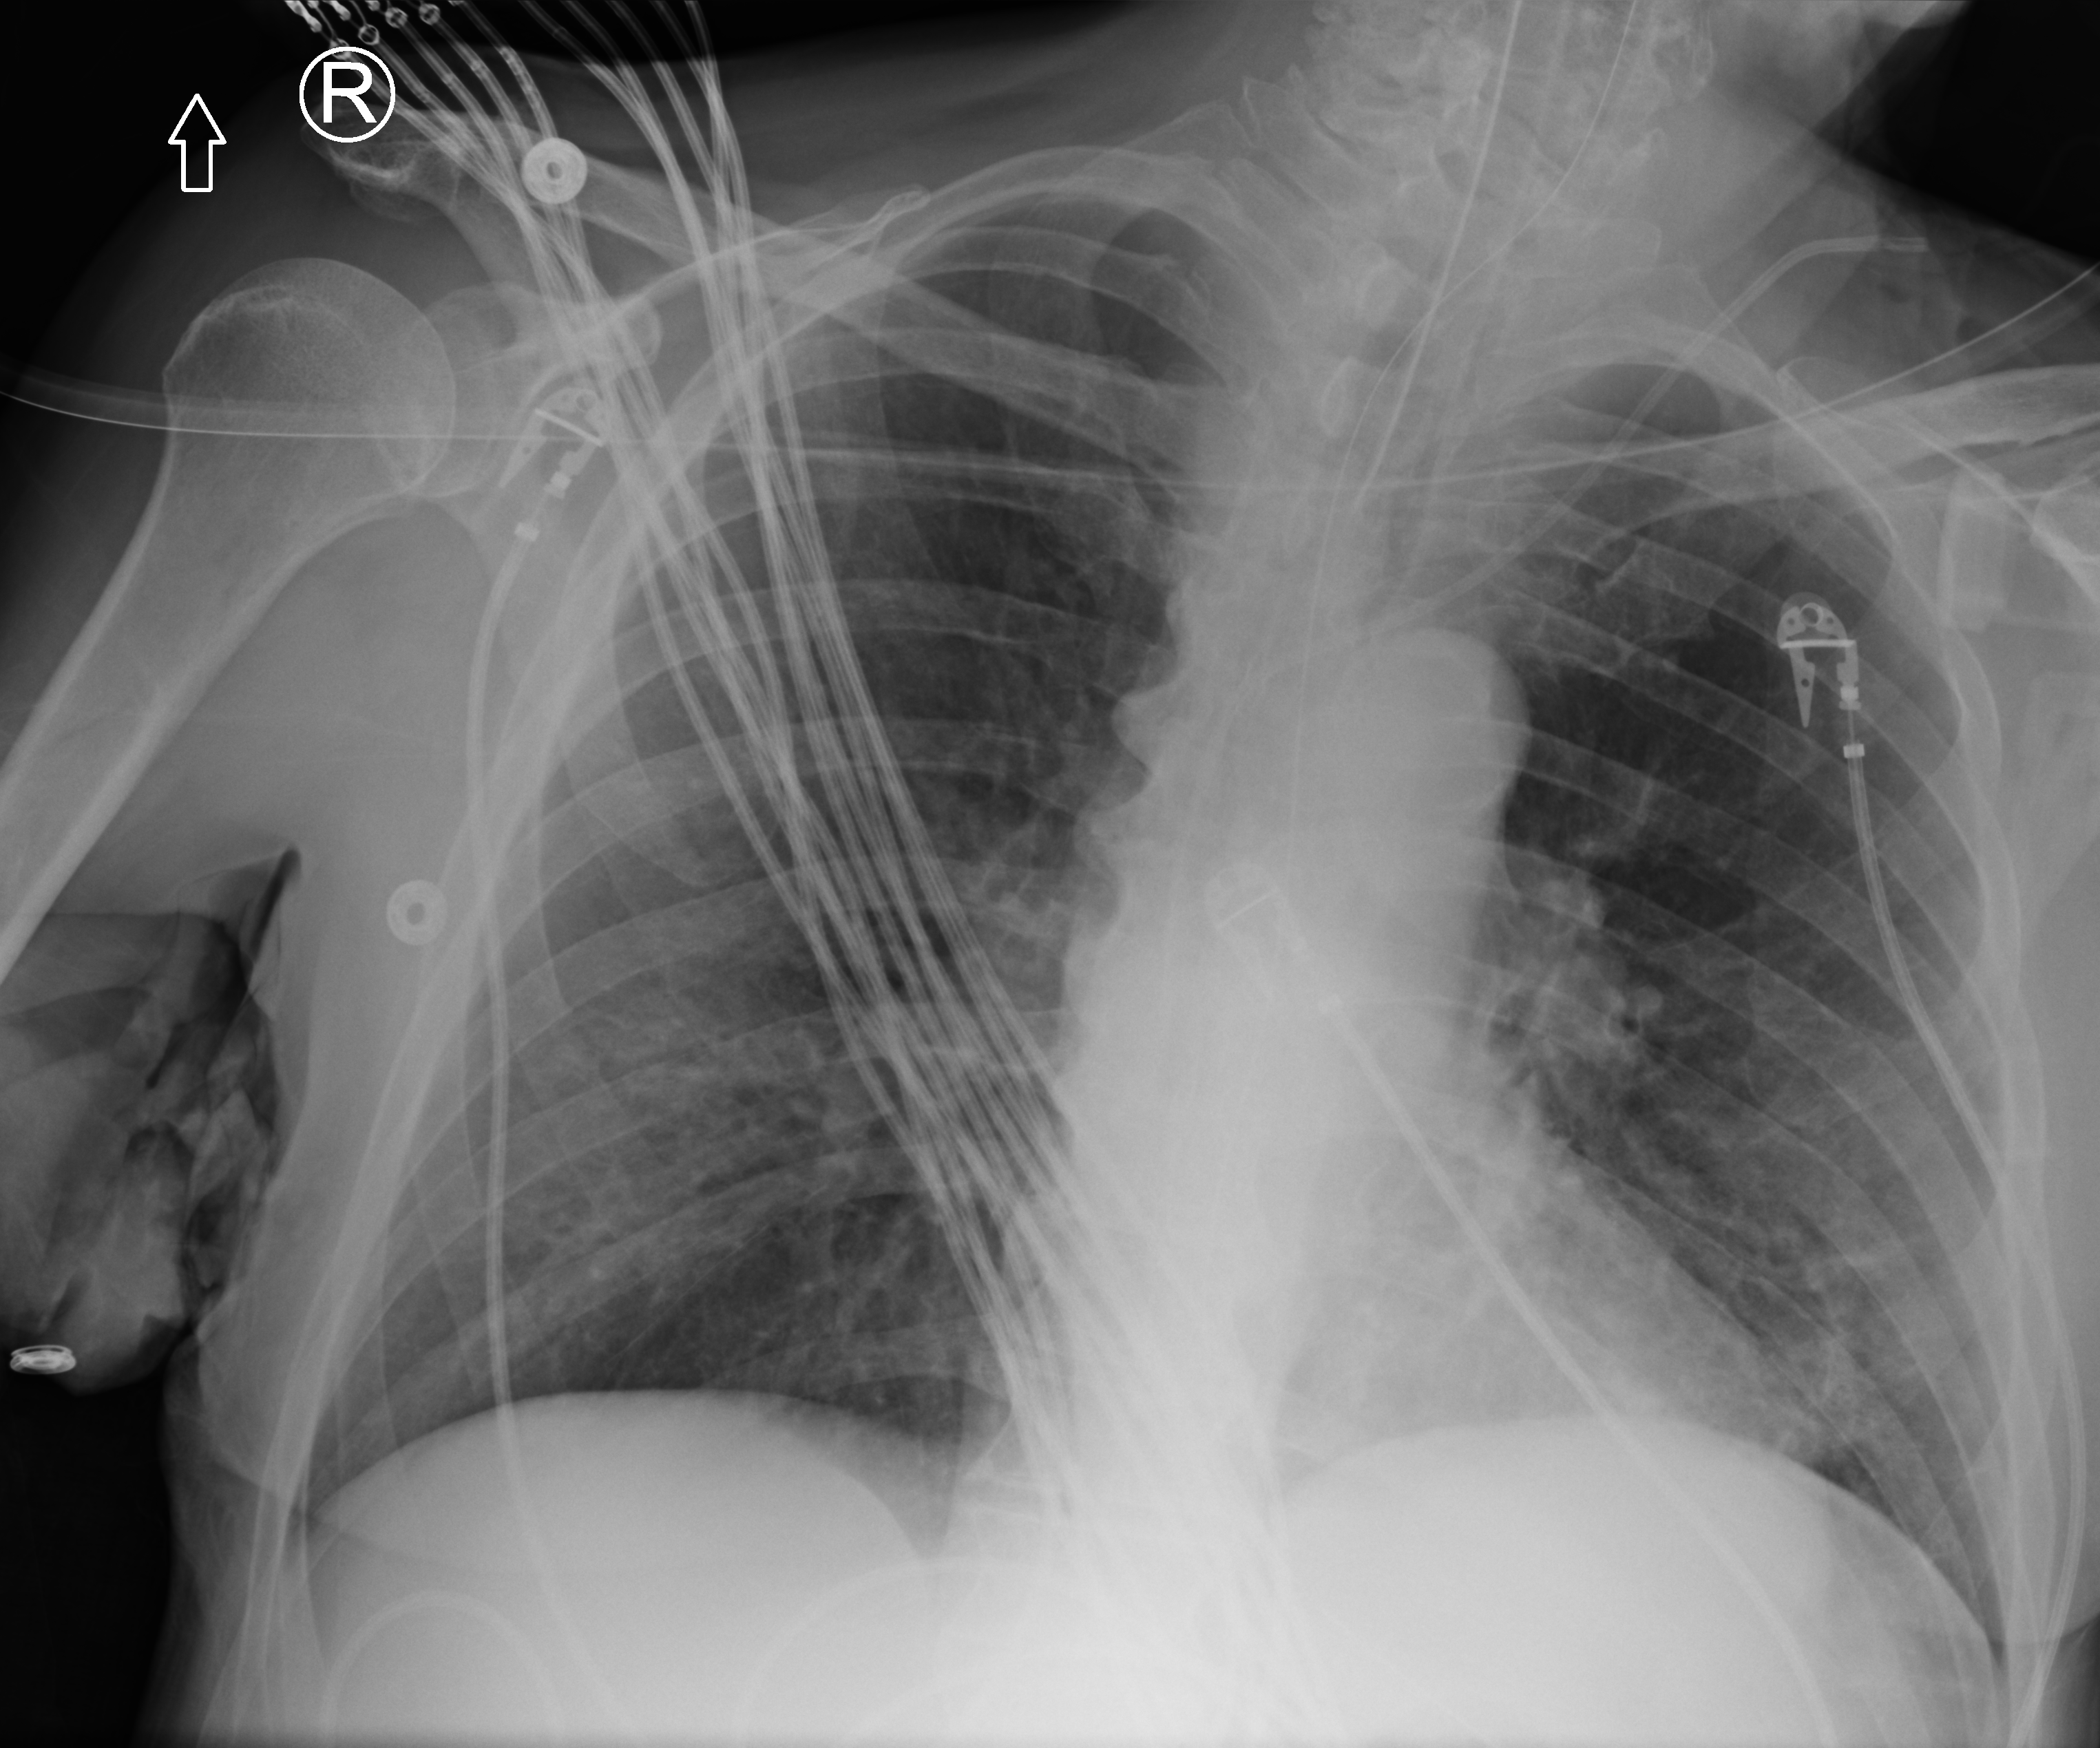
Portable chest radiograph; anteroposterior (AP) projection. Patient hospitalised with COVID-19; male, aged 60–74 years.
Admission-level facts for this patient (not findings on this image; timing relative to this image not recorded): mechanically ventilated during this hospital stay: yes; admitted to intensive care during this hospital stay: yes.